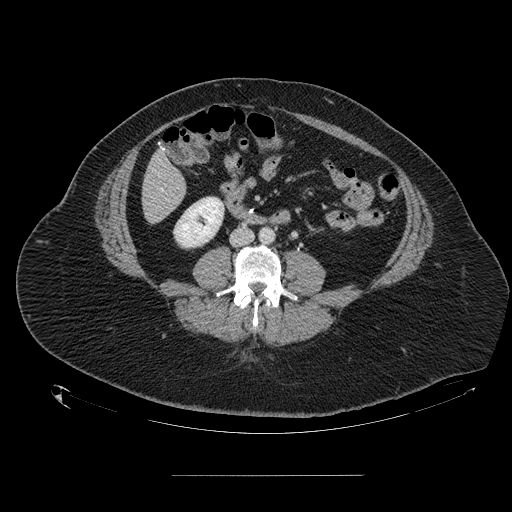
Contrast-enhanced abdominal CT, one axial slice; slice 24 of 164 in the series (ordered by position); 120 kVp; intravenous contrast given; soft-tissue window (W 400 / L 40 HU); 512 × 512 image matrix, field of view 495 × 495 mm. Female patient, age 52 years. From the clinical record (not read from this slice): diagnosis: colorectal cancer liver metastases, imaged before liver resection; multiple liver metastases: yes; largest metastasis: 3.5 cm; disease in both lobes: no.
Annotated regions visible in this slice (manually delineated by an expert):
- hepatic veins: bounding box (x1, y1, x2, y2) in pixels: (161, 189, 163, 191)
- liver: (144, 154, 186, 223)